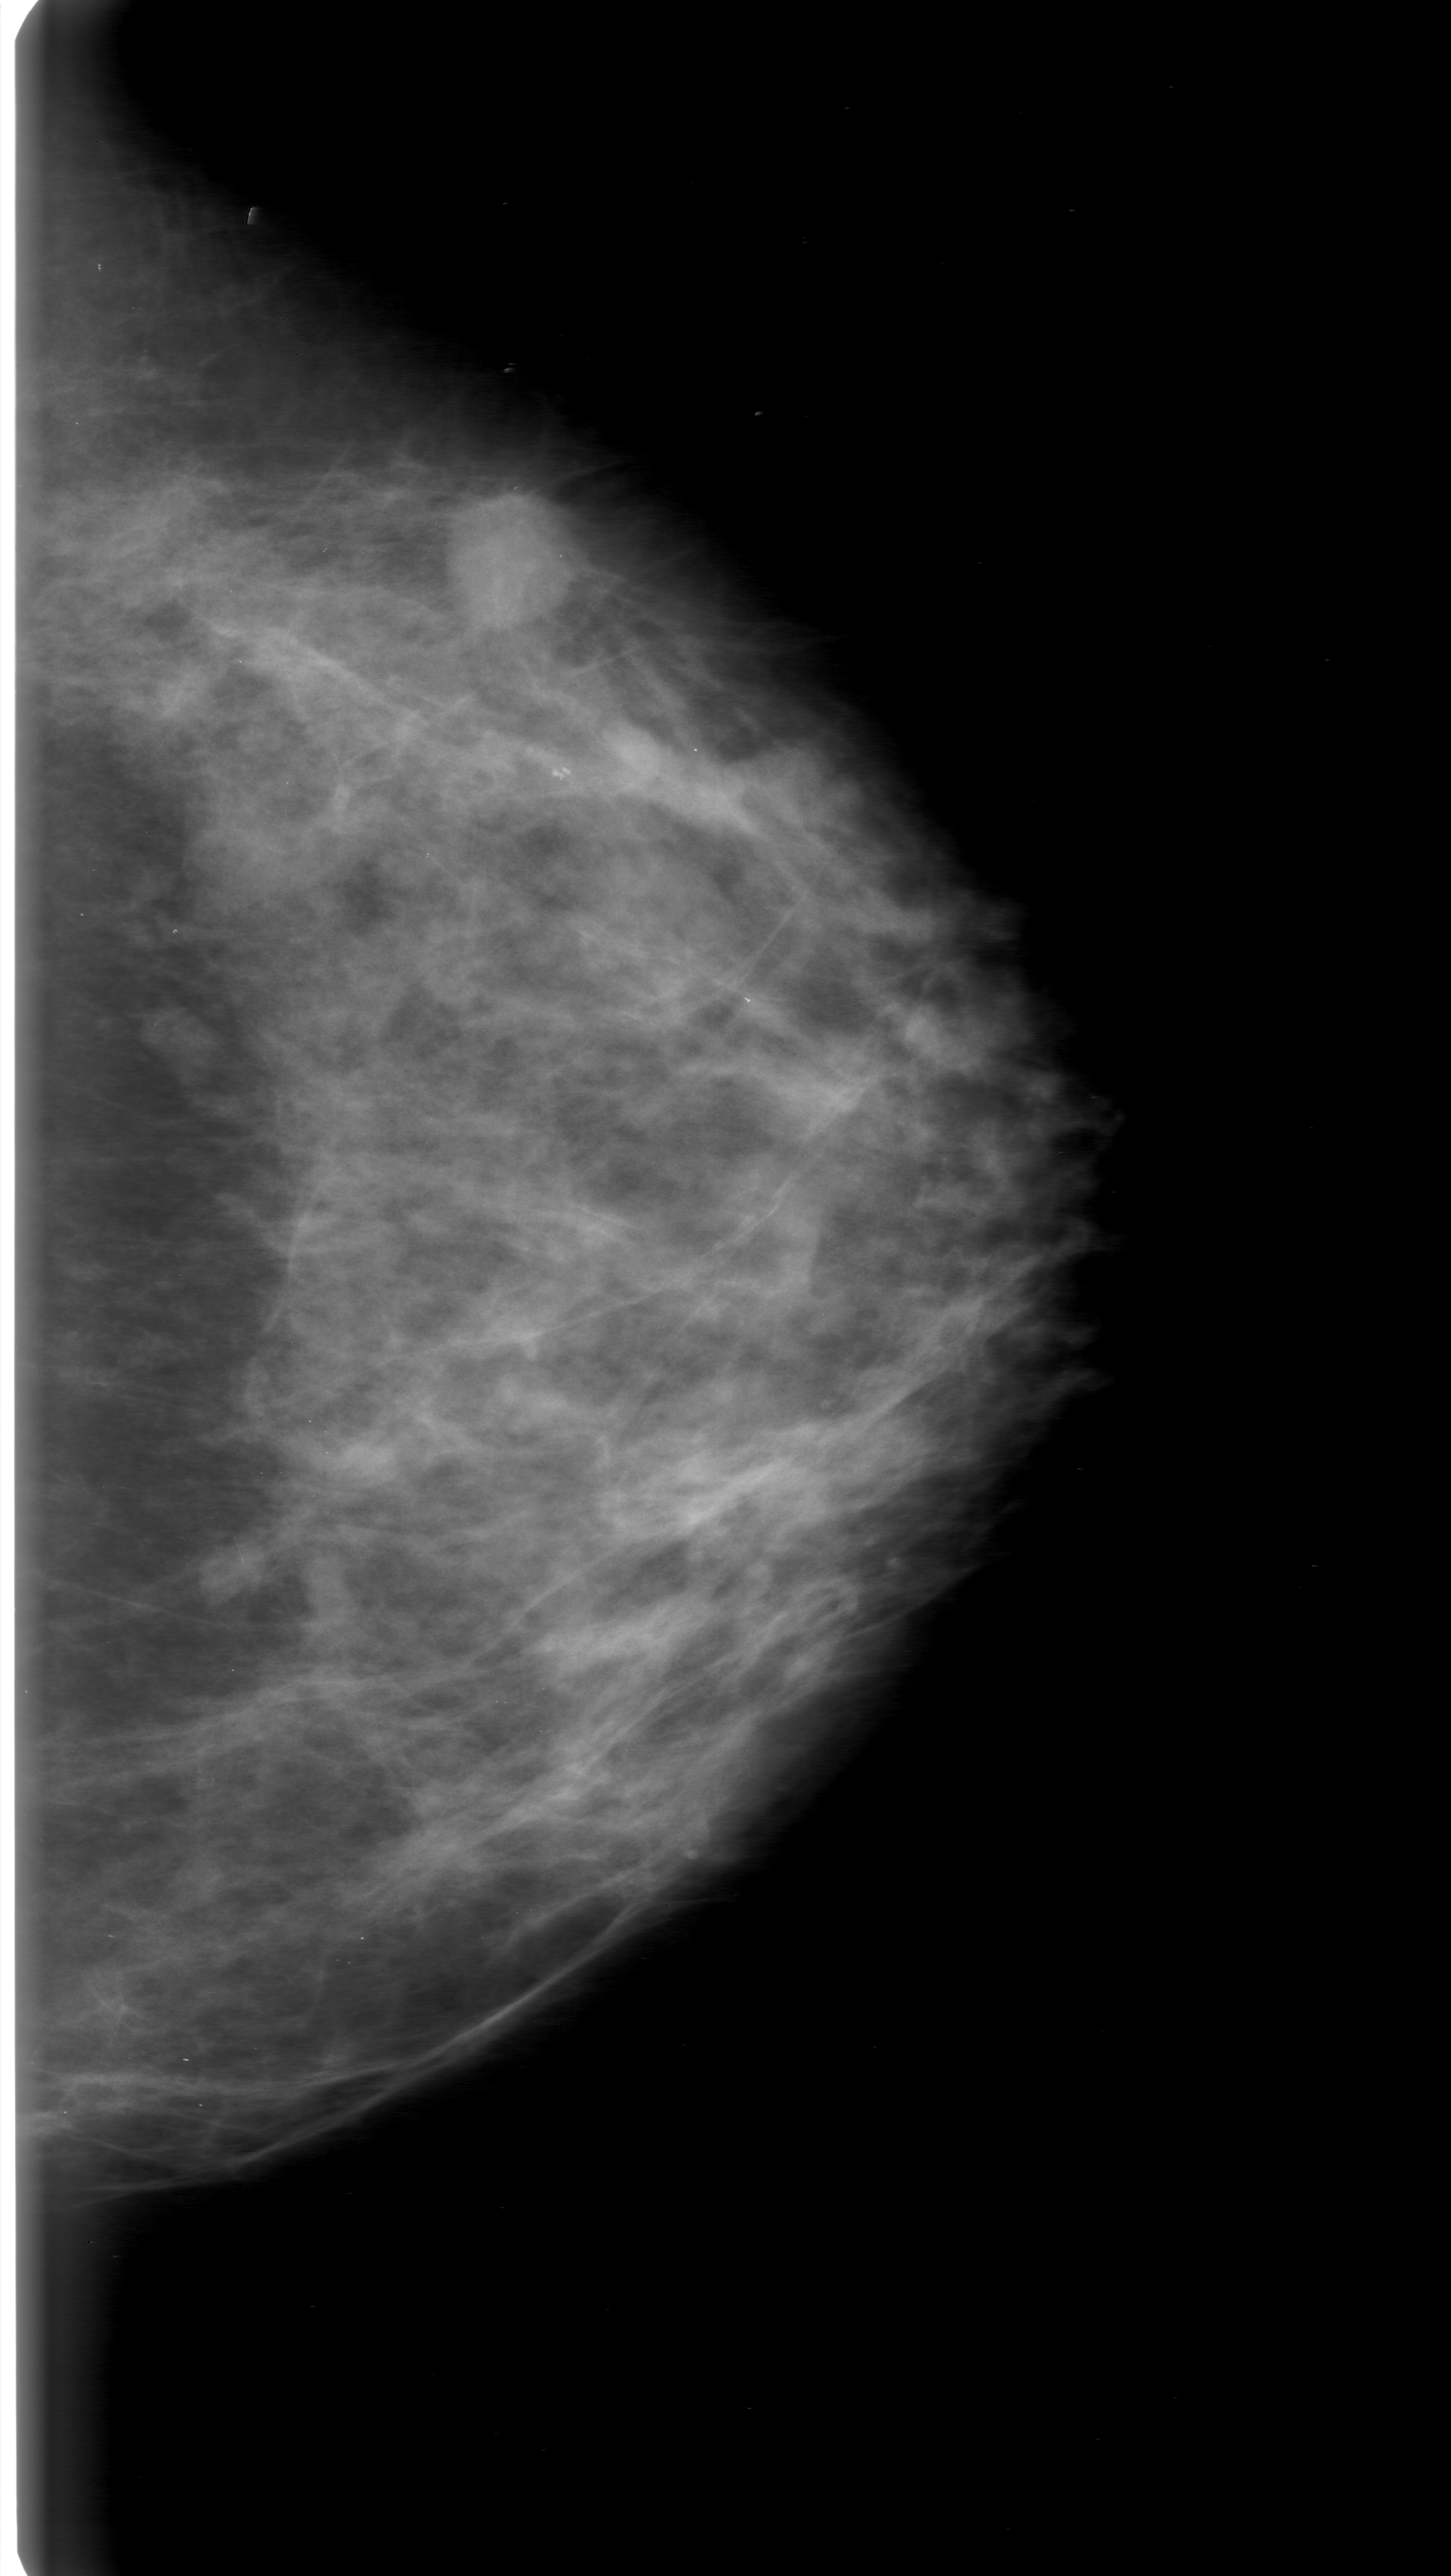
Scanned film-screen mammogram, left breast, CC view, BI-RADS breast density category 3 (scale 1–4).
Marked findings (only marked abnormalities are described; nothing is implied about the rest of the image): mass, shape oval, margins microlobulated; BI-RADS assessment category 0; pathology result (as recorded, not read from the image): malignant.